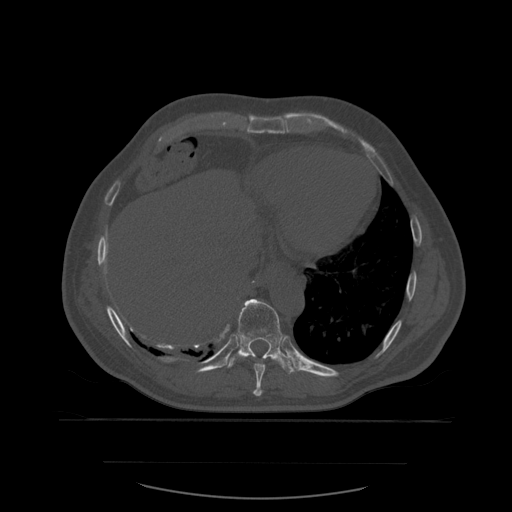
CT including the spine, one axial slice; position 327 of 590 along the scan axis; bone window (W 1800 / L 400 HU); 512 × 512 image matrix, field of view 479 × 479 mm. Patient age 71 years. From the clinical record (not read from this slice): primary cancer: lung; vertebrae with lytic lesions (as recorded): T1, T2, L5, S1.
Annotated regions visible in this slice (semi-automatic segmentation, software-assisted and operator-edited):
- T10 vertebra: bounding box [x1, y1, x2, y2] px = [227, 299, 298, 375]
- T9 vertebra: [253, 358, 266, 397]